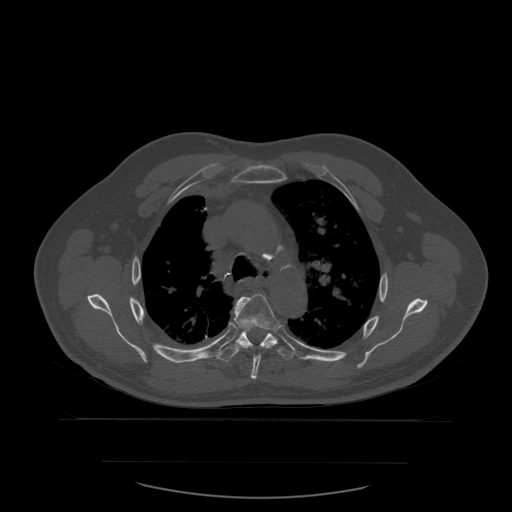
CT including the spine, one axial slice; position 416 of 590 along the scan axis; bone window (W 1800 / L 400 HU); 1.25 mm slice thickness; 512 × 512 image matrix. Patient age 71 years. Case-level facts recorded for this patient, not image findings: primary cancer: lung.
Annotated regions visible in this slice (semi-automatically segmented with operator editing):
- T5 vertebra: bounding box <234,294,279,380> (left, top, right, bottom; pixels)
- T6 vertebra: <218,327,294,362>